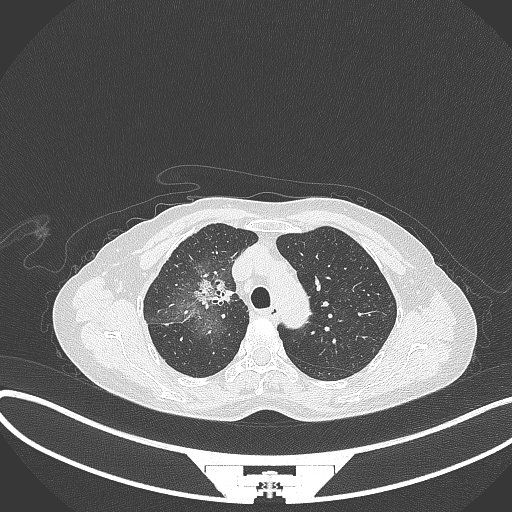
Chest CT, one axial slice. Slice 233 of 284 in the series (ordered by position). 120 kVp. Lung window (W 1500 / L -600 HU). 1 mm slice thickness. 512 × 512 image matrix, field of view 400 × 400 mm. Female patient, age 59 years. From the clinical record (not read from this slice): clinical TNM (as recorded): T3 N0 M0.
Structures marked on this image (rectangle marked by the reading radiologist):
- lung tumour (recorded histology: adenocarcinoma): bounding box (x1, y1, x2, y2) in pixels: (191, 277, 236, 312)